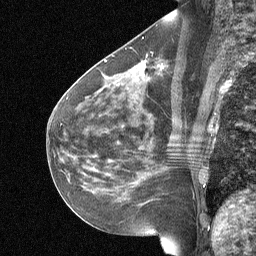
Breast MRI (dynamic contrast-enhanced), one sagittal slice; slice 31 of 64 in the series (ordered by position); dynamic contrast-enhanced study with each time point stored as its own series, time point 2 of 3 at this slice position (early post-contrast, ordered by acquisition time); 1.5 T; TE 4.8 ms, TR 27 ms; 2 mm slice thickness; 256 × 256 image matrix. Female patient, age 51 years. From the clinical record (not read from this slice): setting: breast cancer imaged before/during neoadjuvant chemotherapy; receptor status: HR-positive, HER2-negative.
Structures marked on this image (semi-automatically segmented with operator editing):
- analysis volume of interest (the breast-tissue region the enhancement analysis was run in; not a lesion): bounding box (x1, y1, x2, y2) in pixels: (88, 42, 186, 119)
- tumour enhancement mask (voxels above the 90 % enhancement threshold inside the analysis volume of interest): (140, 64, 145, 69)